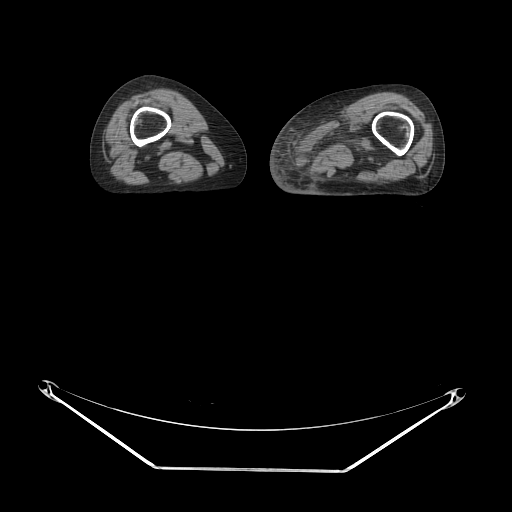
CT of an extremity soft-tissue mass (from a PET/CT study), one axial slice; position 6 of 91 along the scan axis; 140 kVp; soft-tissue window (W 400 / L 40 HU); 3.75 mm slice thickness; 512 × 512 image matrix, field of view 500 × 500 mm. Female patient. From the clinical record (not read from this slice): histological type: pleomorphic leiomyosarcoma; grade: high; site of the primary tumour: left thigh.
Structures marked on this image (expert contour drawn on MRI and transferred to this co-registered scan by the dataset authors):
- gross tumour volume including surrounding oedema: bounding box [x1, y1, x2, y2] px = [302, 110, 384, 175]